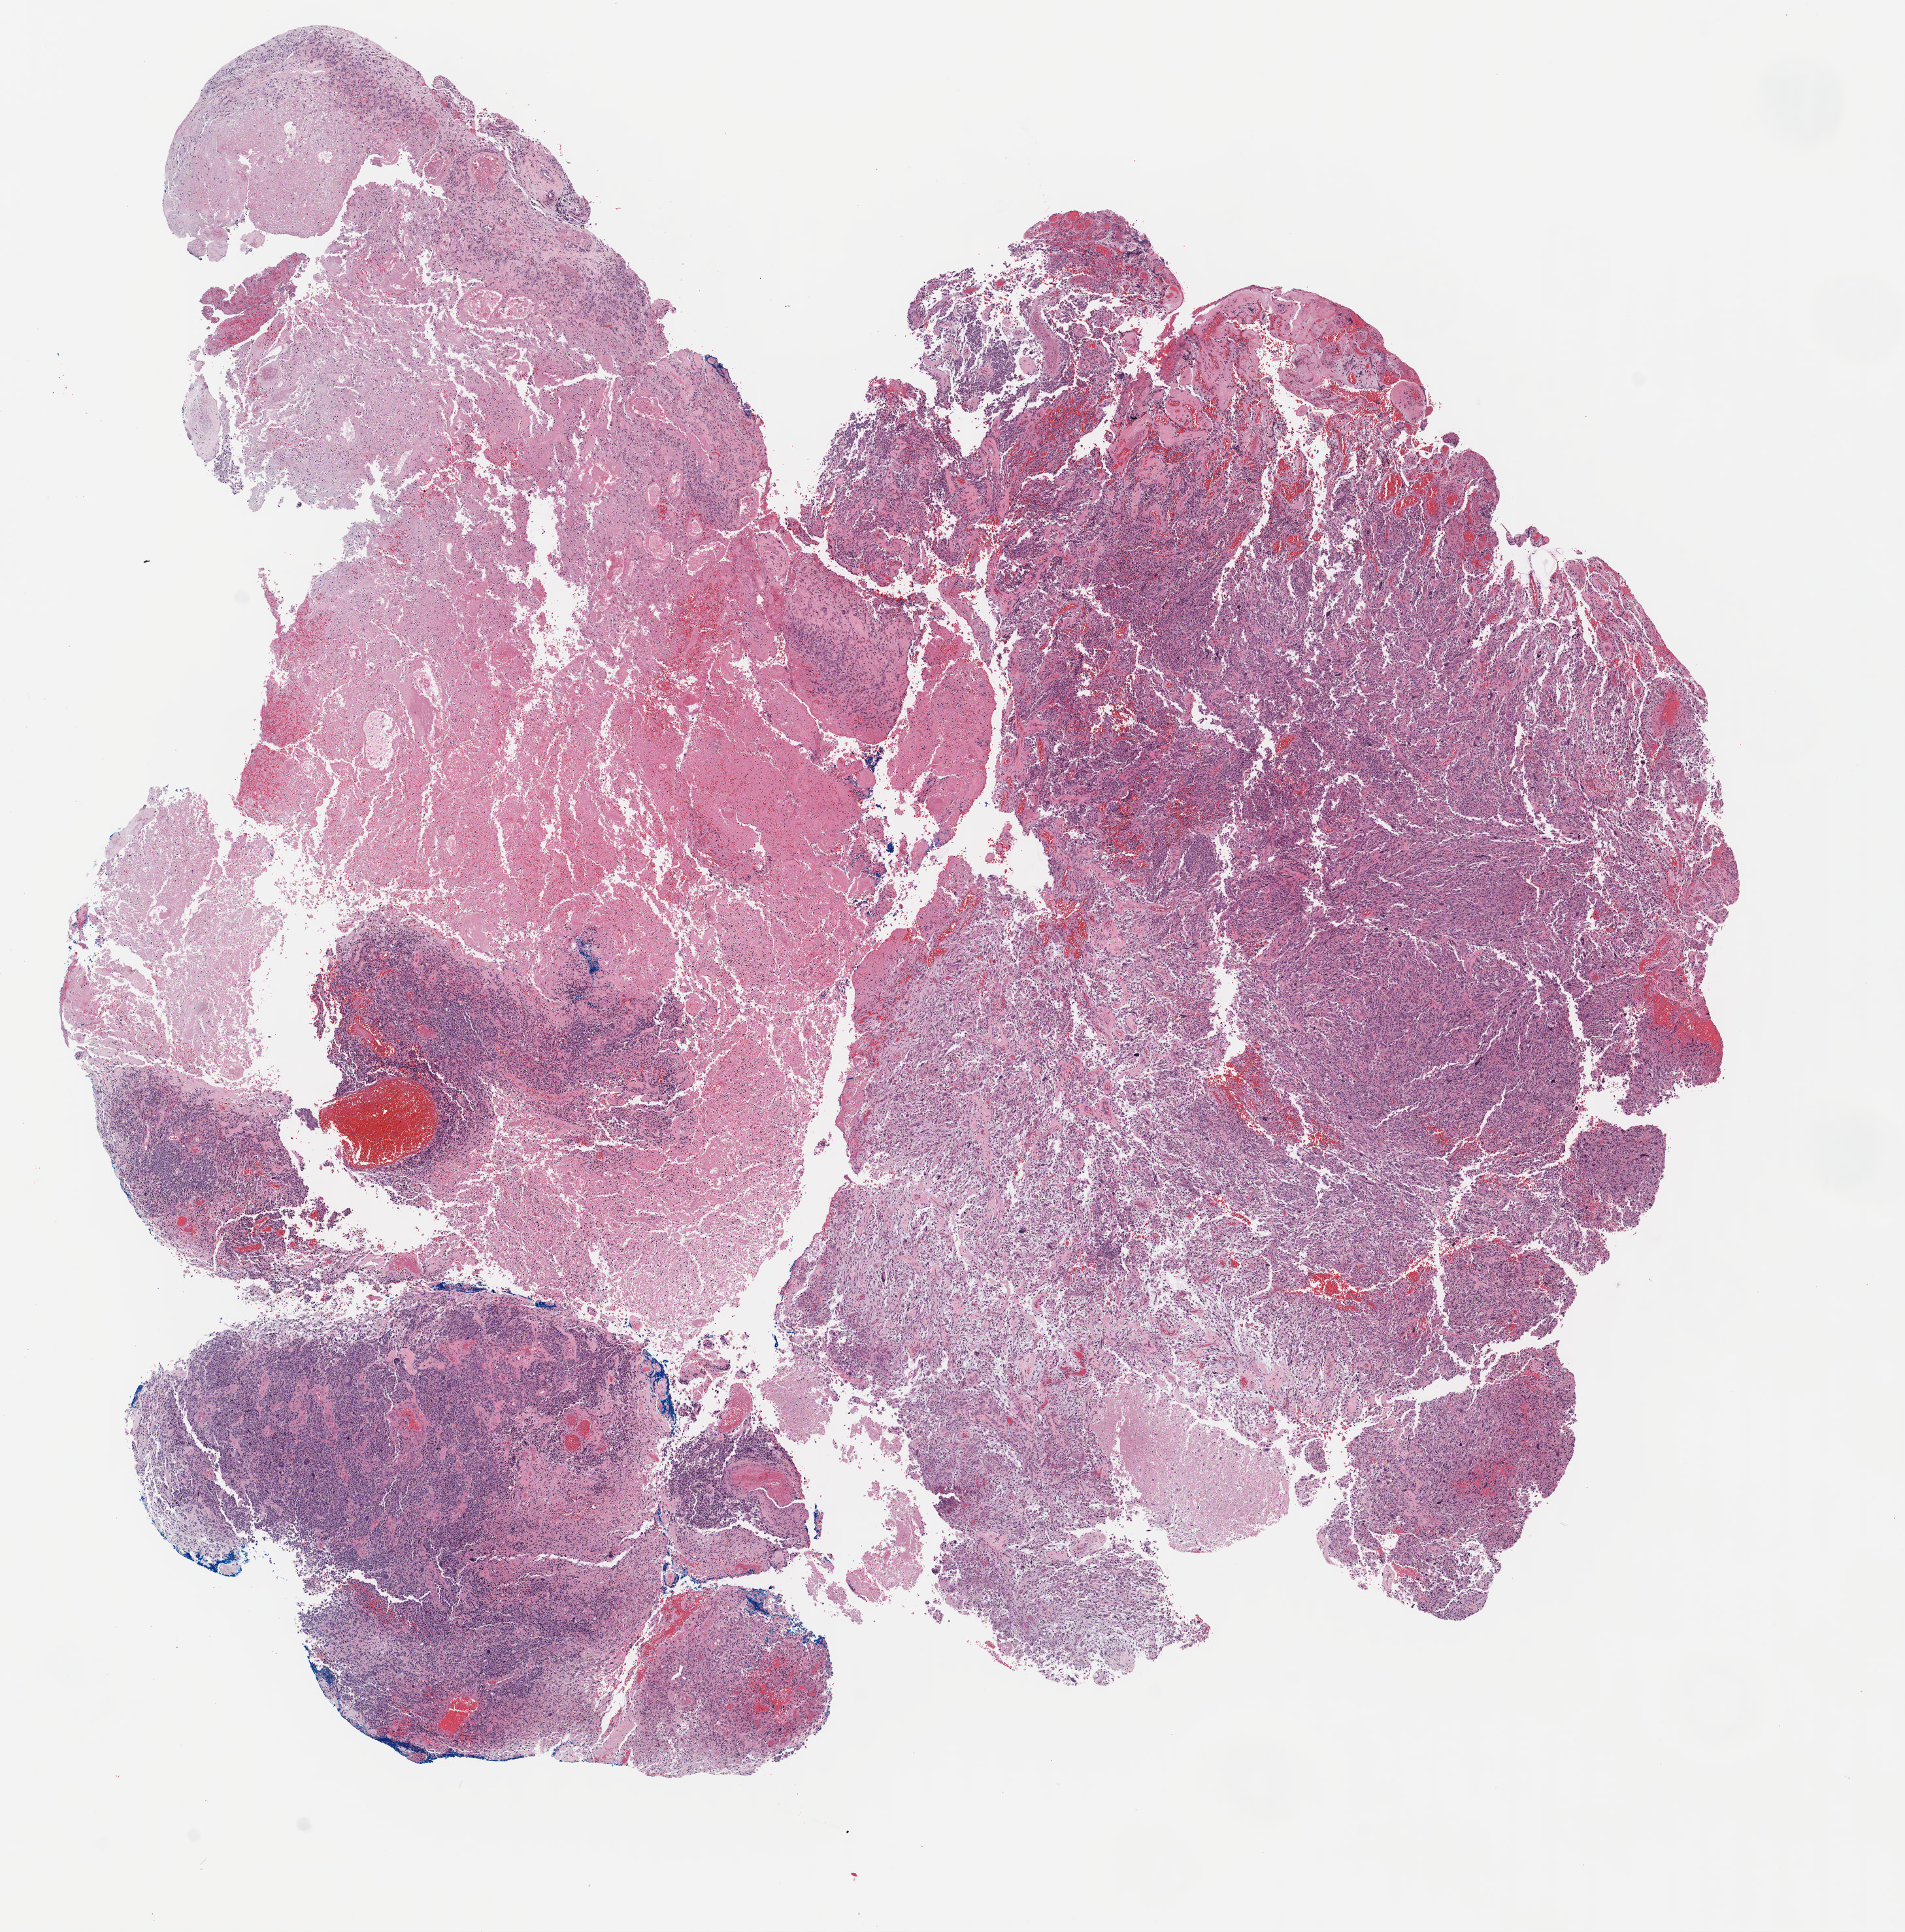
Digitized Hematoxylin and eosin (H&E) stained tissue section (whole slide) — low-resolution overview of the scanned area, about 11.5 x 11.6 mm, formalin-fixed paraffin-embedded (FFPE) diagnostic section, primary tumour sample from the brain. Male, age 39 years at initial diagnosis.
Diagnosis: Glioblastoma.